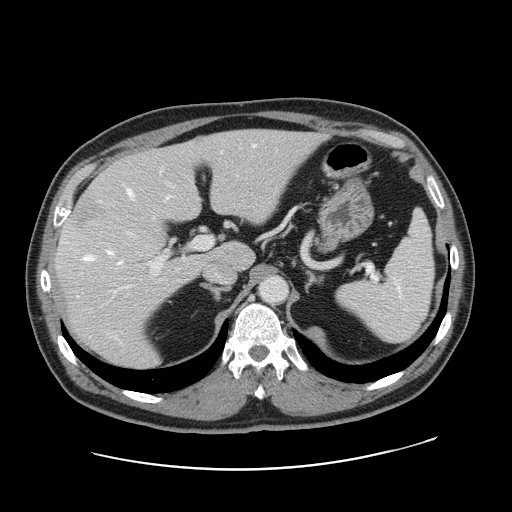
Contrast-enhanced abdominal CT, one axial slice. Slice 107 of 178 in the series (ordered by position). Intravenous contrast given. Soft-tissue window (W 400 / L 40 HU). 2.5 mm slice thickness. 512 × 512 image matrix, field of view 403 × 403 mm. Male patient, age 63 years. From the clinical record (not read from this slice): diagnosis: colorectal cancer liver metastases, imaged before liver resection; multiple liver metastases: yes; largest metastasis: 8 cm; disease in both lobes: yes.
Annotated regions visible in this slice (outlined manually by an expert reader):
- hepatic veins: bounding box <84,145,255,264> (left, top, right, bottom; pixels)
- liver: <56,129,318,369>
- planned liver remnant (the part of the liver to remain after resection): <127,129,318,270>
- portal vein (with intrahepatic branches): <127,199,213,271>
- liver metastasis: <71,205,106,228>